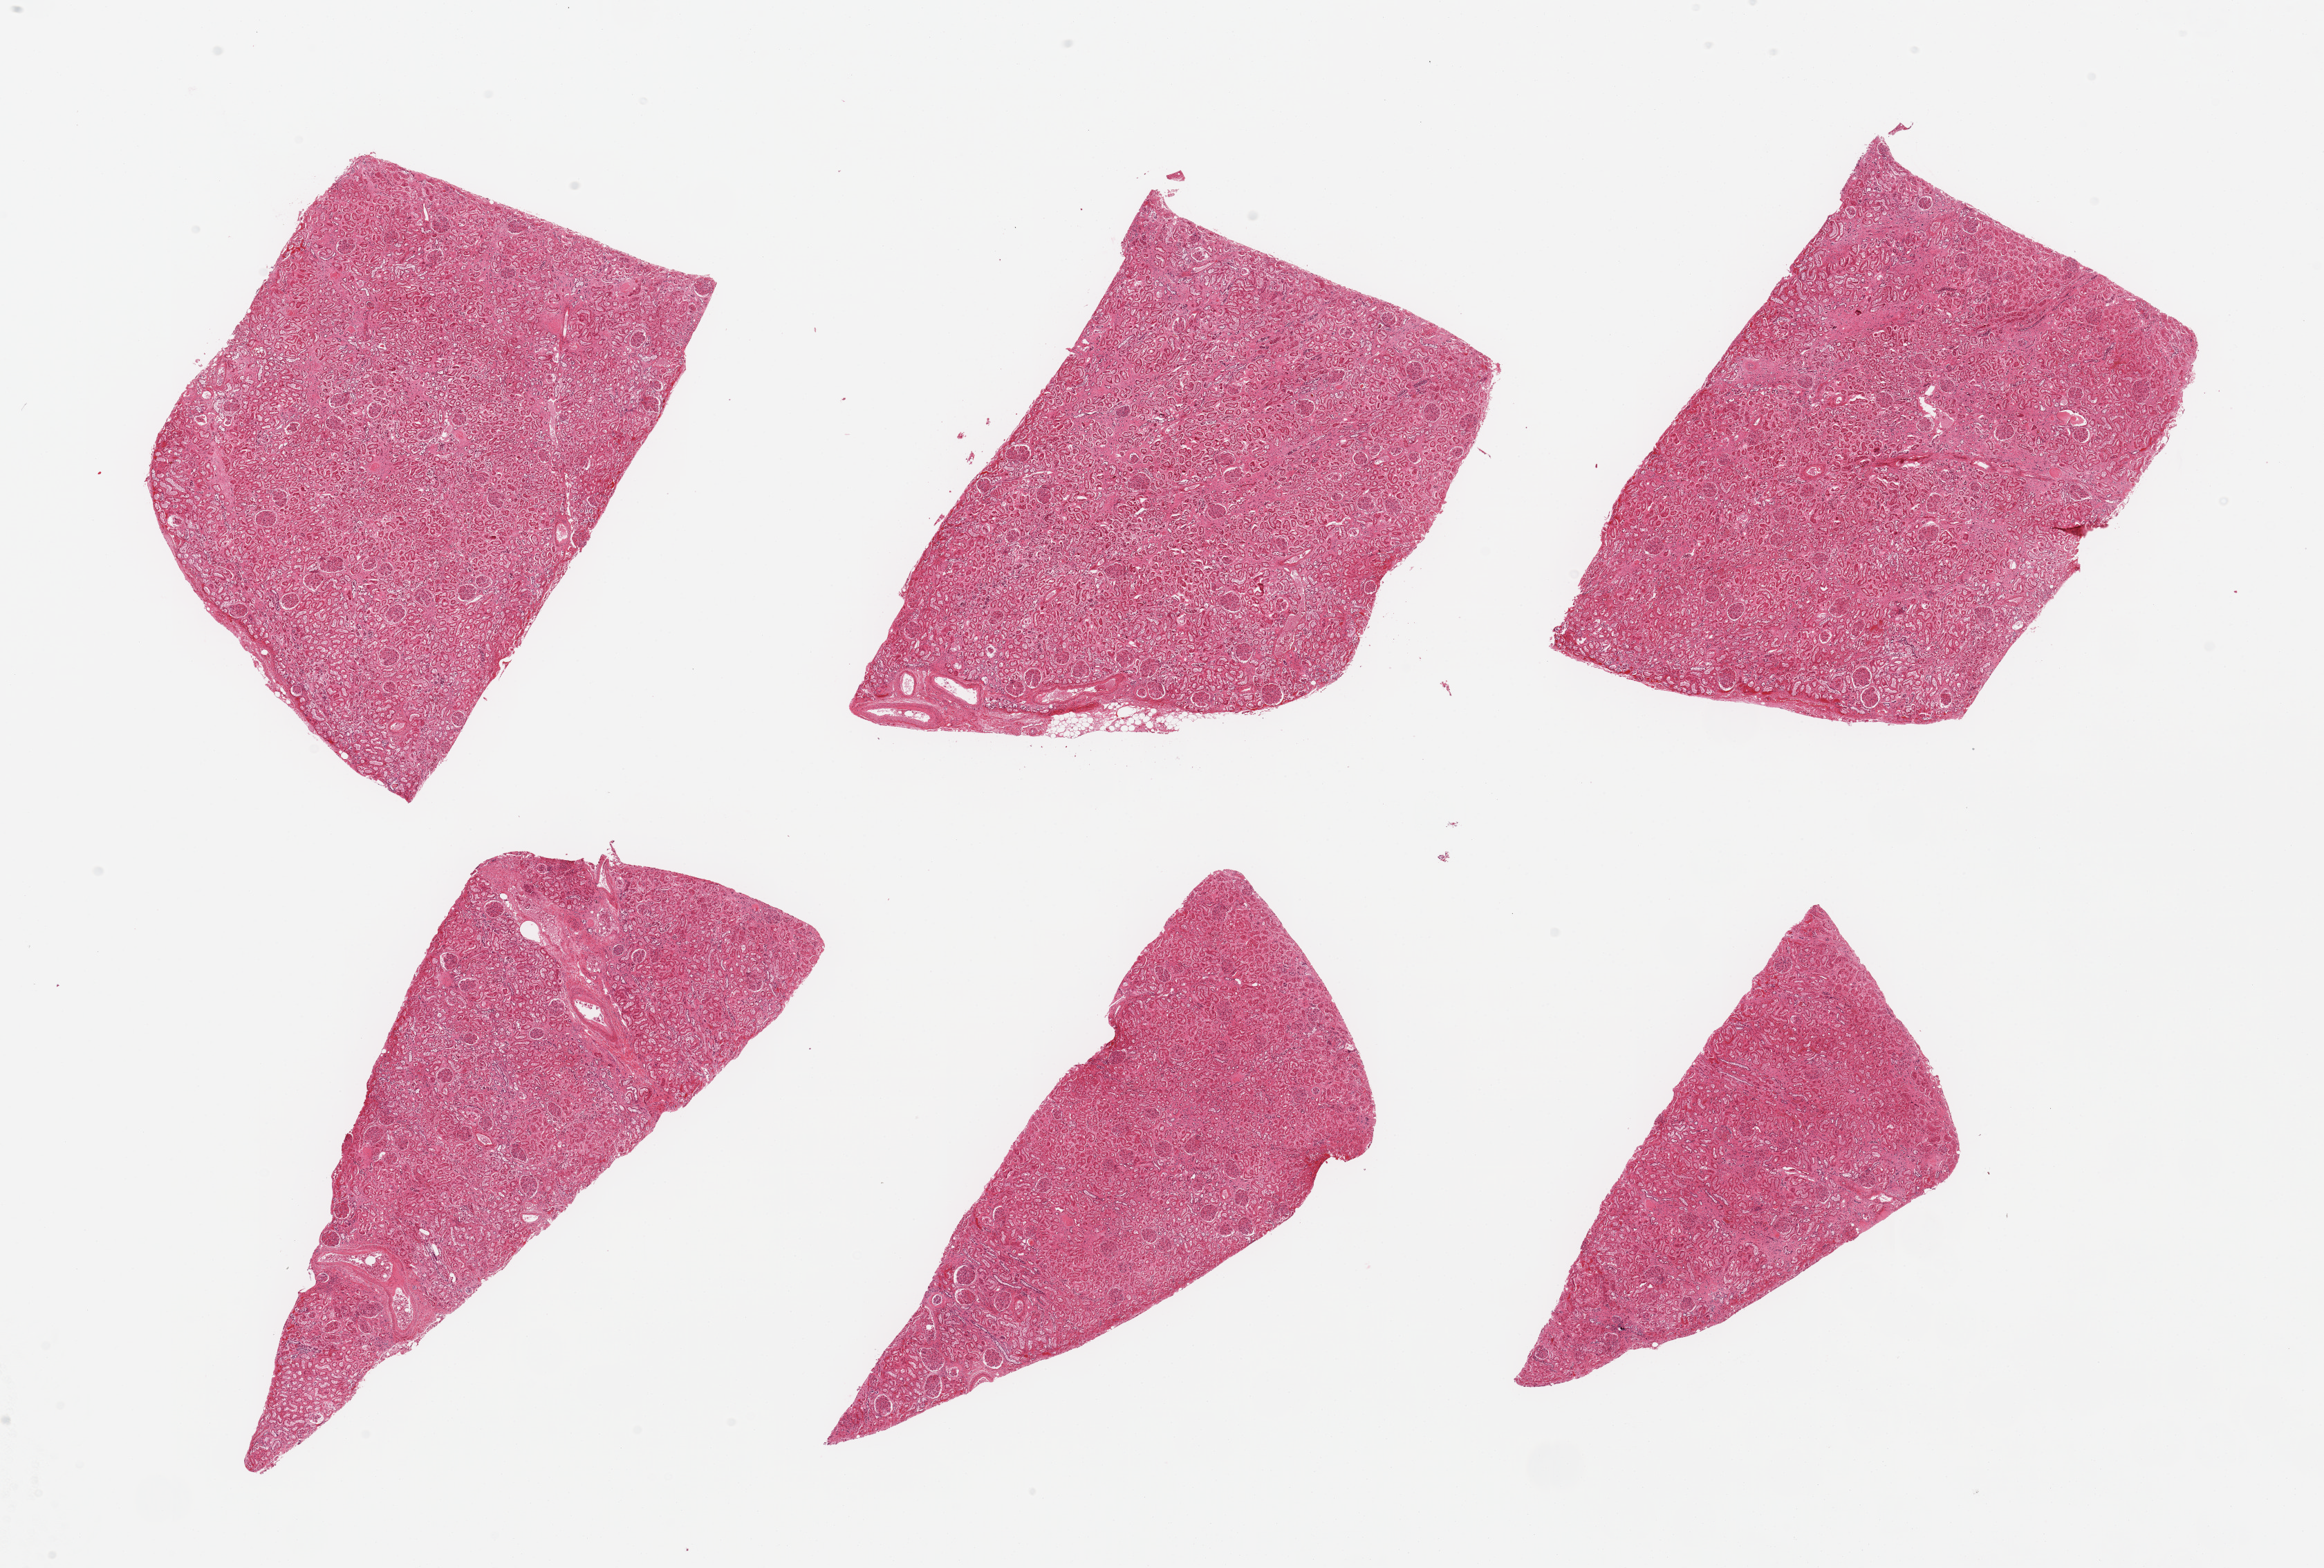
Whole-slide image, haematoxylin and eosin stain, whole scanned area (about 26.6 x 17.9 mm, slide scanned at 20x) shown as a low-resolution overview; PAXgene-fixed, paraffin-embedded tissue; sampled site (target tissue): renal cortex; donor tissue sample. Donor sex: male.
• pathologist's review note for this sample: 6 pieces; renal cortex with patchy interstitial fibrosis and hyalinized glomeruli